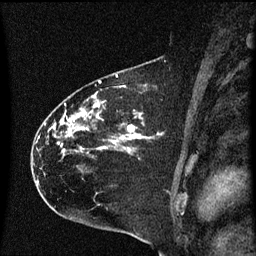
Breast MRI (dynamic contrast-enhanced), one sagittal slice. Slice 42 of 60 in the series (ordered by position). Dynamic contrast-enhanced series, image 2 of 3 at this slice position (ordered by acquisition). 1.5 T. TE 4.2 ms, TR 8.4 ms. 2 mm slice thickness. 256 × 256 image matrix, field of view 200 × 200 mm. Patient: female, 35 years. Case-level facts recorded for this patient, not image findings: setting: breast cancer imaged before/during neoadjuvant chemotherapy; receptor status: HER2-positive.
Structures marked on this image (semi-automatic segmentation, software-assisted and operator-edited):
- analysis volume of interest (the breast-tissue region the enhancement analysis was run in; not a lesion): bounding box <34,68,166,173> (left, top, right, bottom; pixels)
- tumour enhancement mask (voxels above the 70 % enhancement threshold inside the analysis volume of interest): <38,76,159,151>